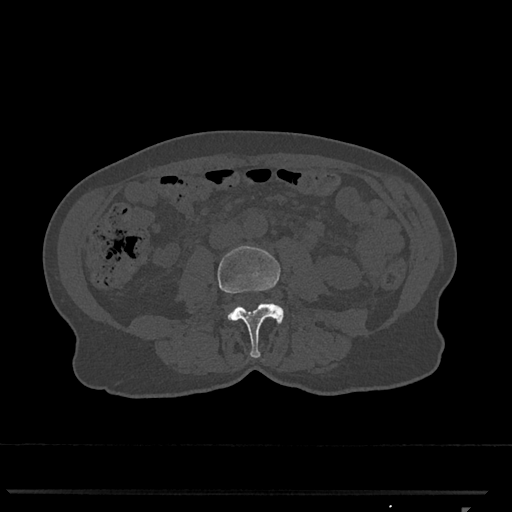
CT including the spine, one axial slice; slice 261 of 793 in the series (ordered by position); reconstruction kernel Br40s/3; 120 kVp; bone window (W 1800 / L 400 HU); 0.5 mm slice thickness; 512 × 512 image matrix, field of view 380 × 380 mm. Female patient, age 62 years. From the clinical record (not read from this slice): primary cancer: renal.
Structures marked on this image (semi-automatically segmented with operator editing):
- L3 vertebra: bounding box [x1, y1, x2, y2] px = [217, 246, 284, 358]